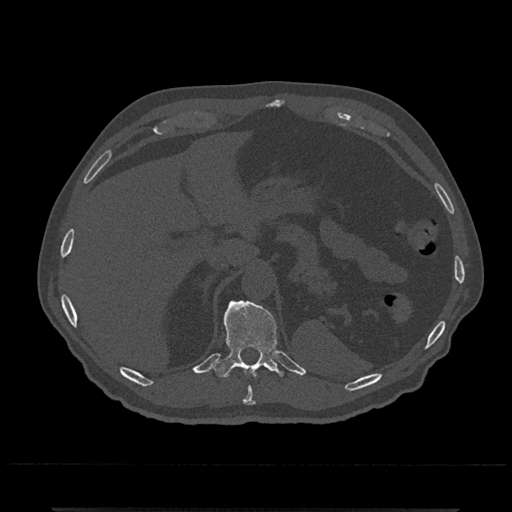
CT including the spine, one axial slice. Position 506 of 797 along the scan axis. Reconstruction kernel Br40s/3. Bone window (W 1800 / L 400 HU). 0.5 mm slice thickness. 512 × 512 image matrix, field of view 393 × 393 mm. Male patient, age 67 years. Case-level facts recorded for this patient, not image findings: primary cancer: prostate.
Annotated regions visible in this slice (semi-automatic segmentation, software-assisted and operator-edited):
- T10 vertebra: bounding box (x1, y1, x2, y2) in pixels: (243, 387, 254, 405)
- T11 vertebra: (213, 300, 284, 378)